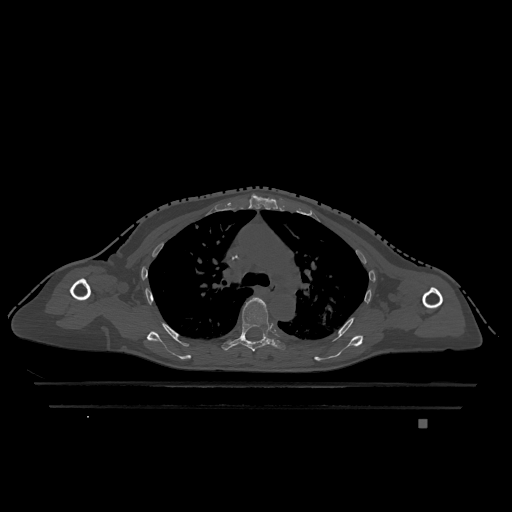
CT including the spine, one axial slice. Slice 841 of 1317 in the series (ordered by position). Bone window (W 1800 / L 400 HU). 512 × 512 image matrix, field of view 500 × 500 mm. Patient: female, 74 years. From the clinical record (not read from this slice): primary cancer: lung; vertebrae with lytic lesions (as recorded): T1, T4, T5, T6, L4, L5.
Outlined on this slice (semi-automatic segmentation, software-assisted and operator-edited):
- T5 vertebra: bounding box [x1, y1, x2, y2] px = [222, 297, 286, 352]